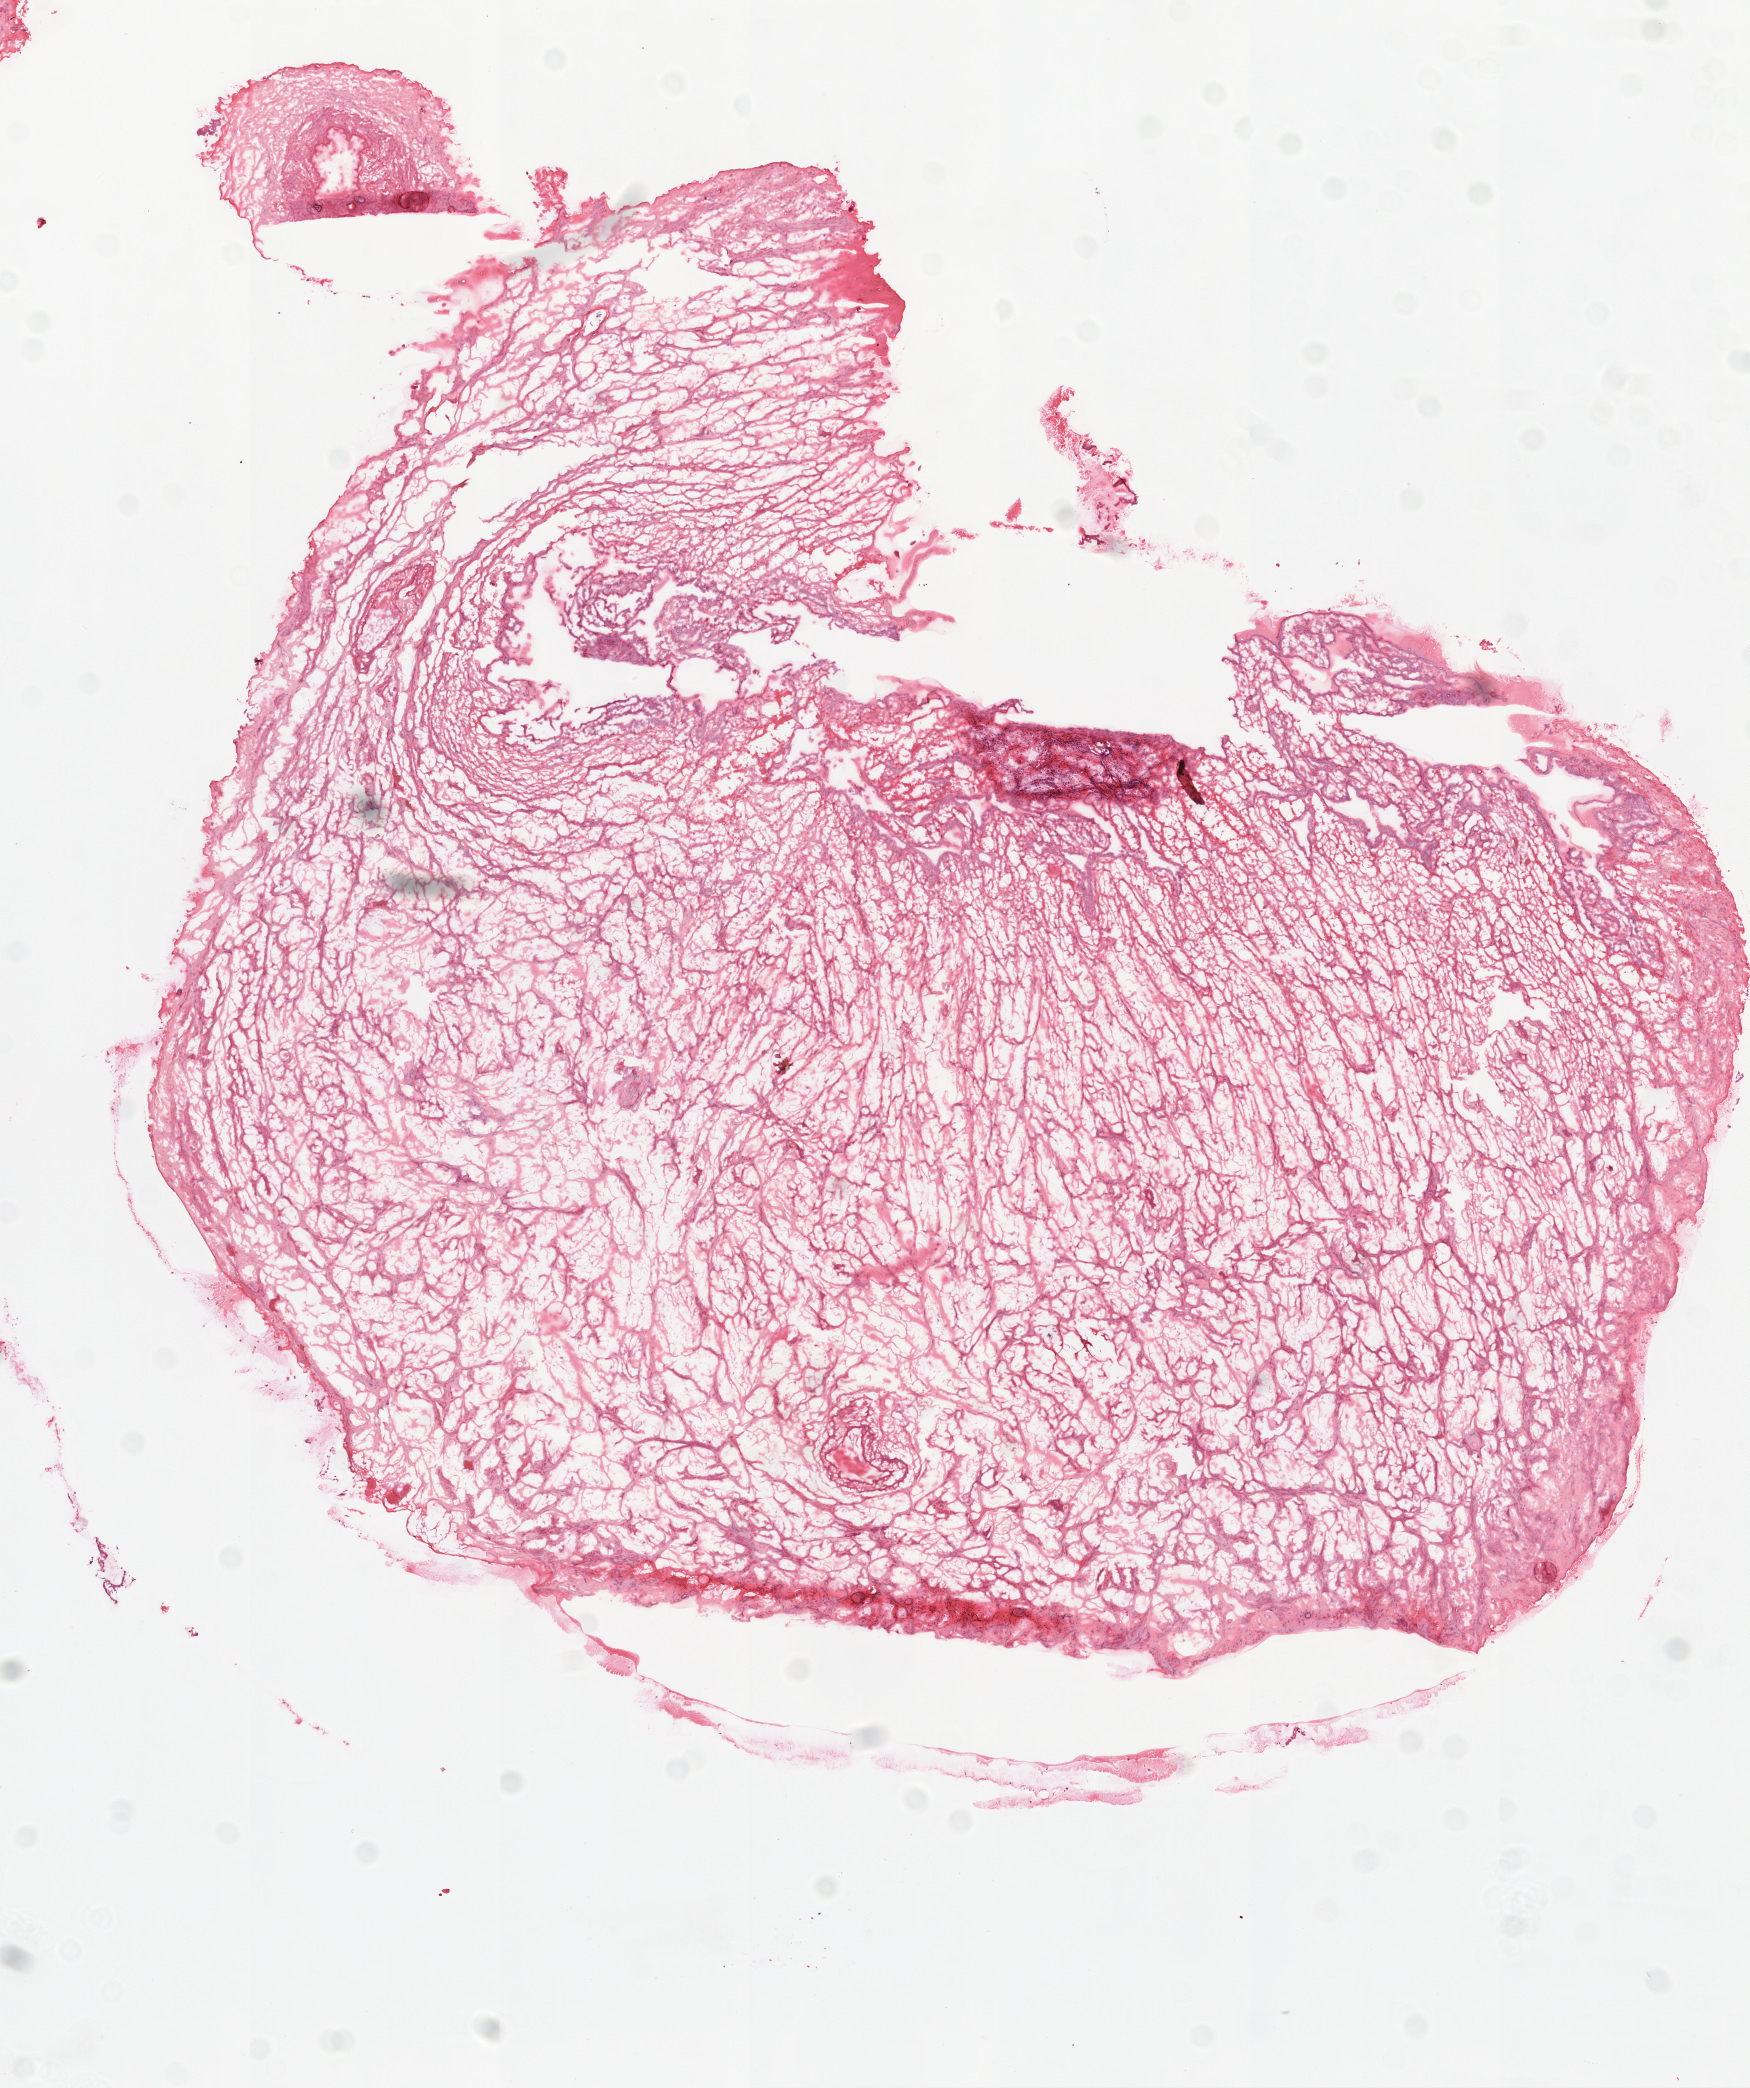
Whole-slide histology image, H&E — shown as a low-resolution overview of the whole scanned area (about 7.0 x 8.4 mm, from a 20x scan); frozen section; ovary, solid tissue normal (non-tumour tissue) sample. Female patient; age at initial diagnosis 55 years.
This section: solid tissue normal sample (biorepository sample class). Patient diagnosis: Serous cystadenocarcinoma, NOS.